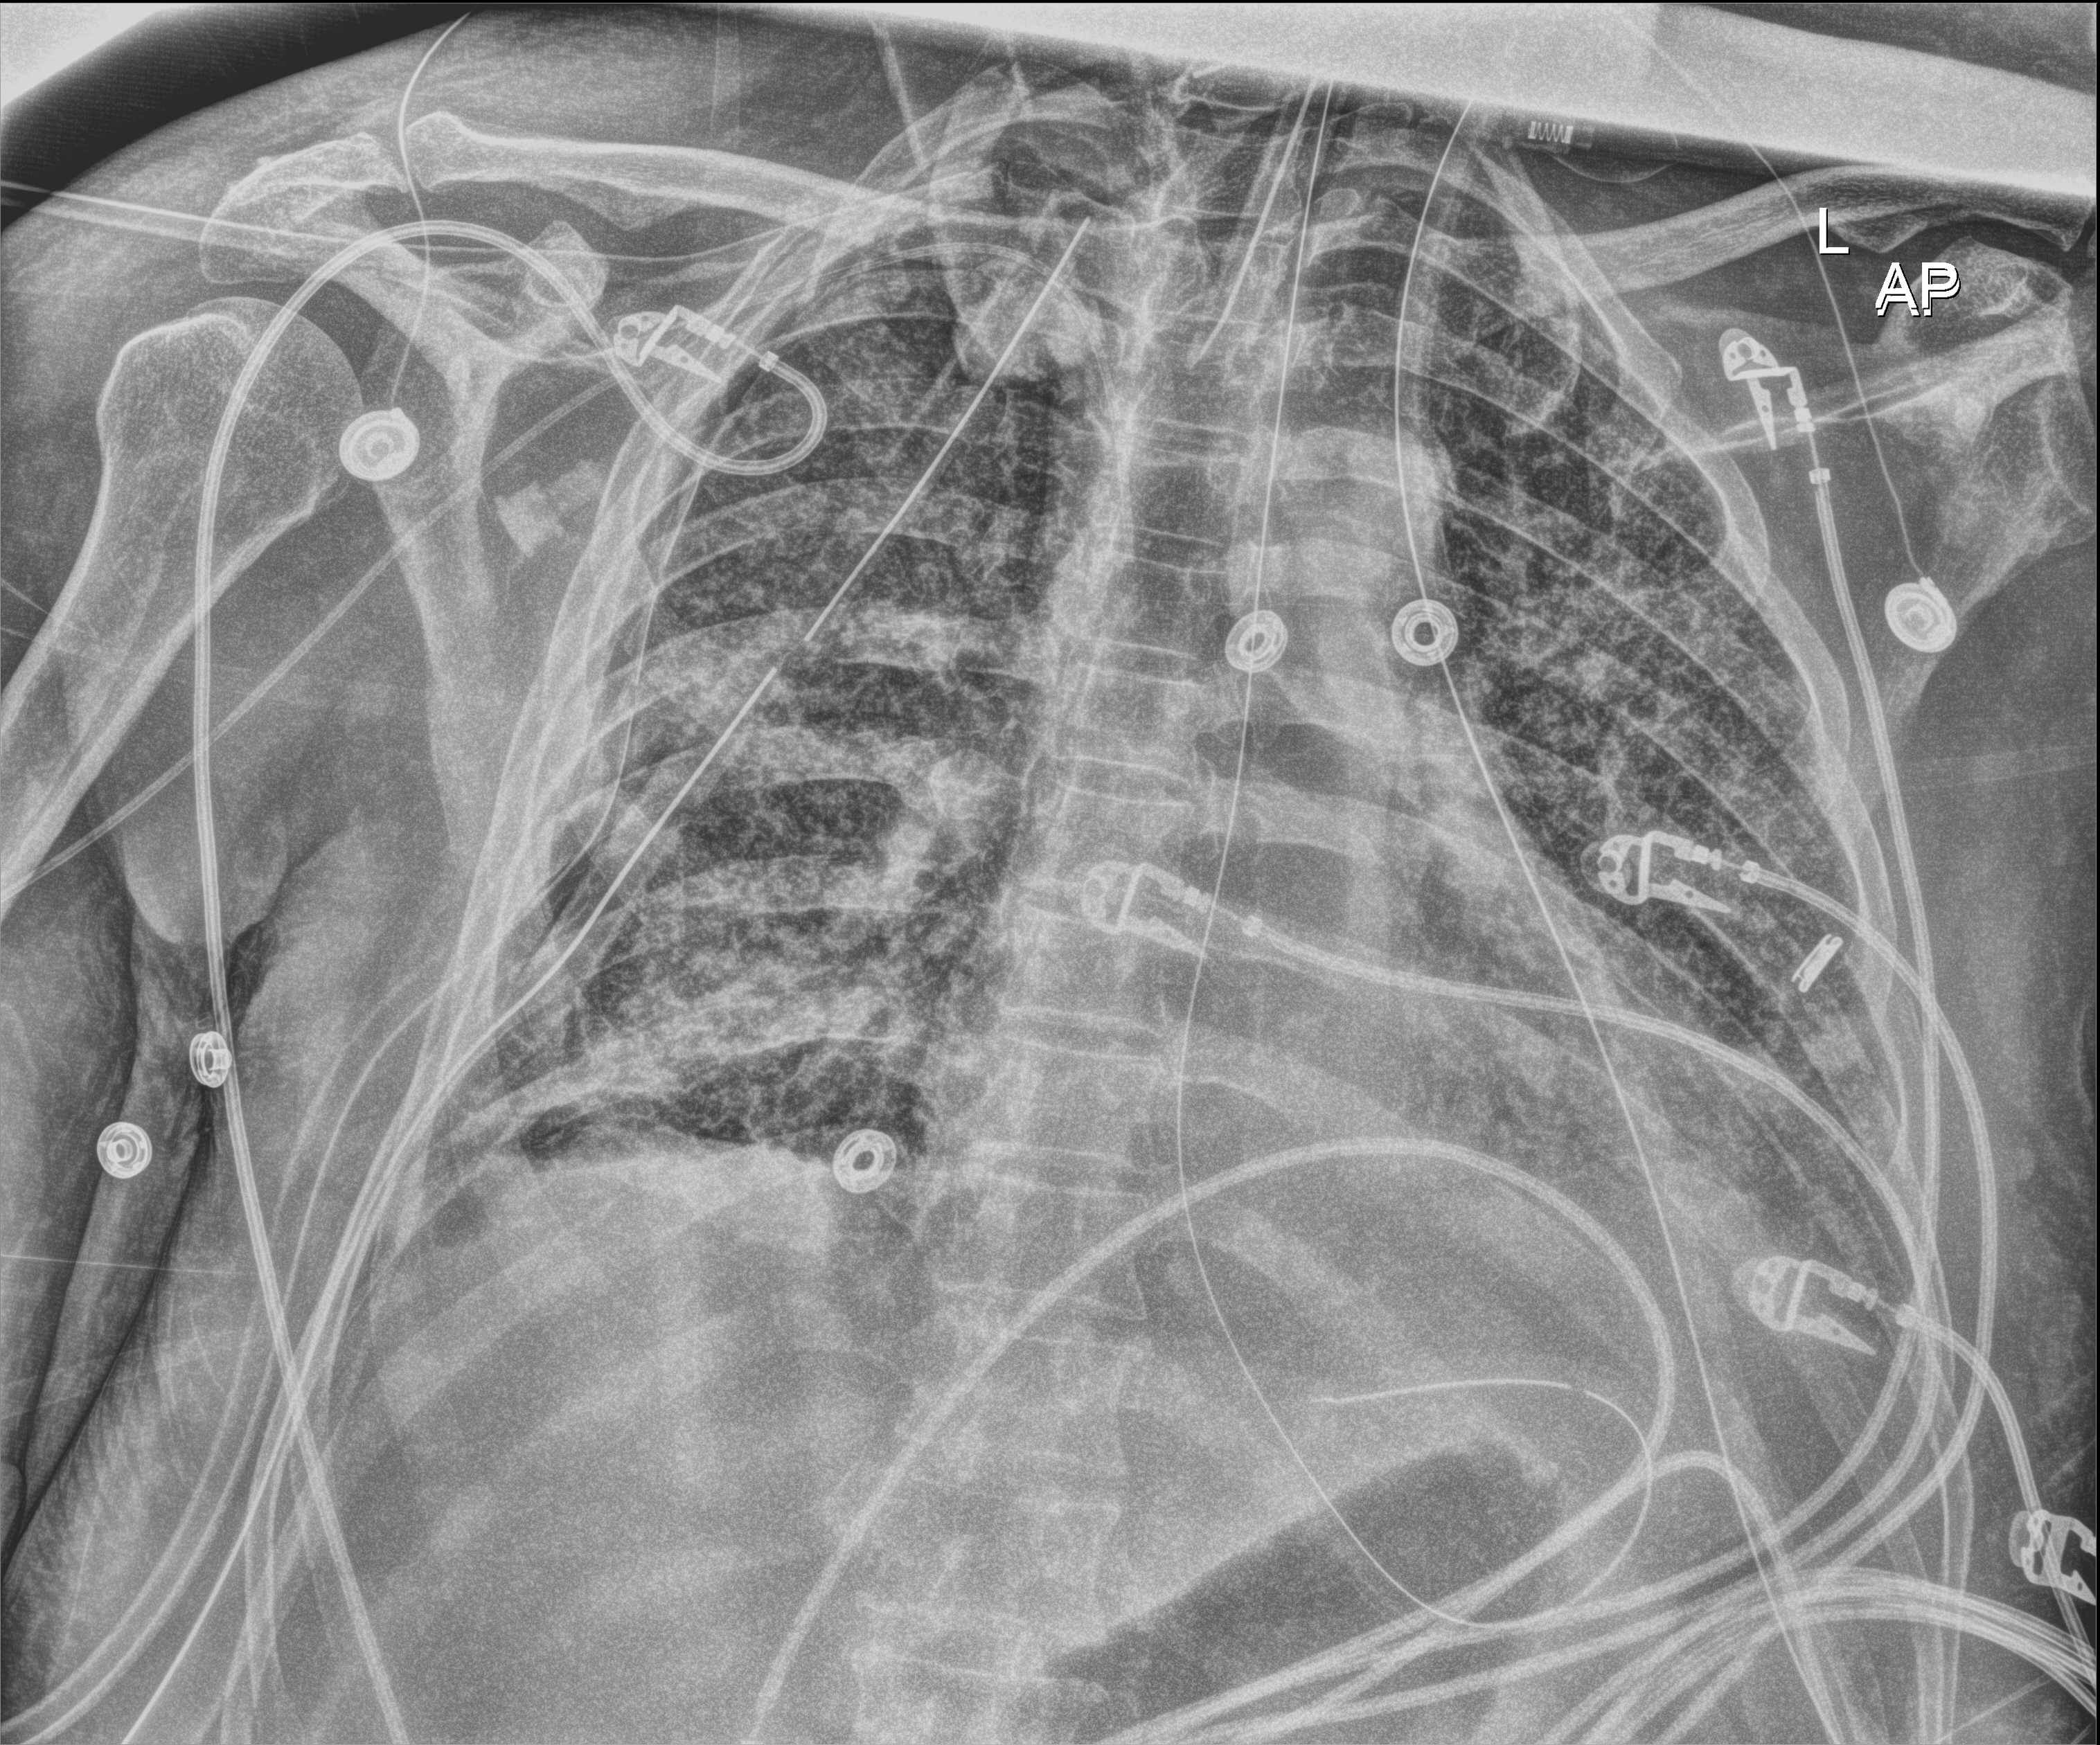
Bedside chest radiograph (digital radiography), anteroposterior (AP) projection. Patient hospitalised with COVID-19; male, aged 60–74 years.
Hospital-stay facts (about this admission, not read from this image; timing relative to this image not recorded): admitted to intensive care during this hospital stay: yes; mechanically ventilated during this hospital stay: yes; smoking status (admission record): never.